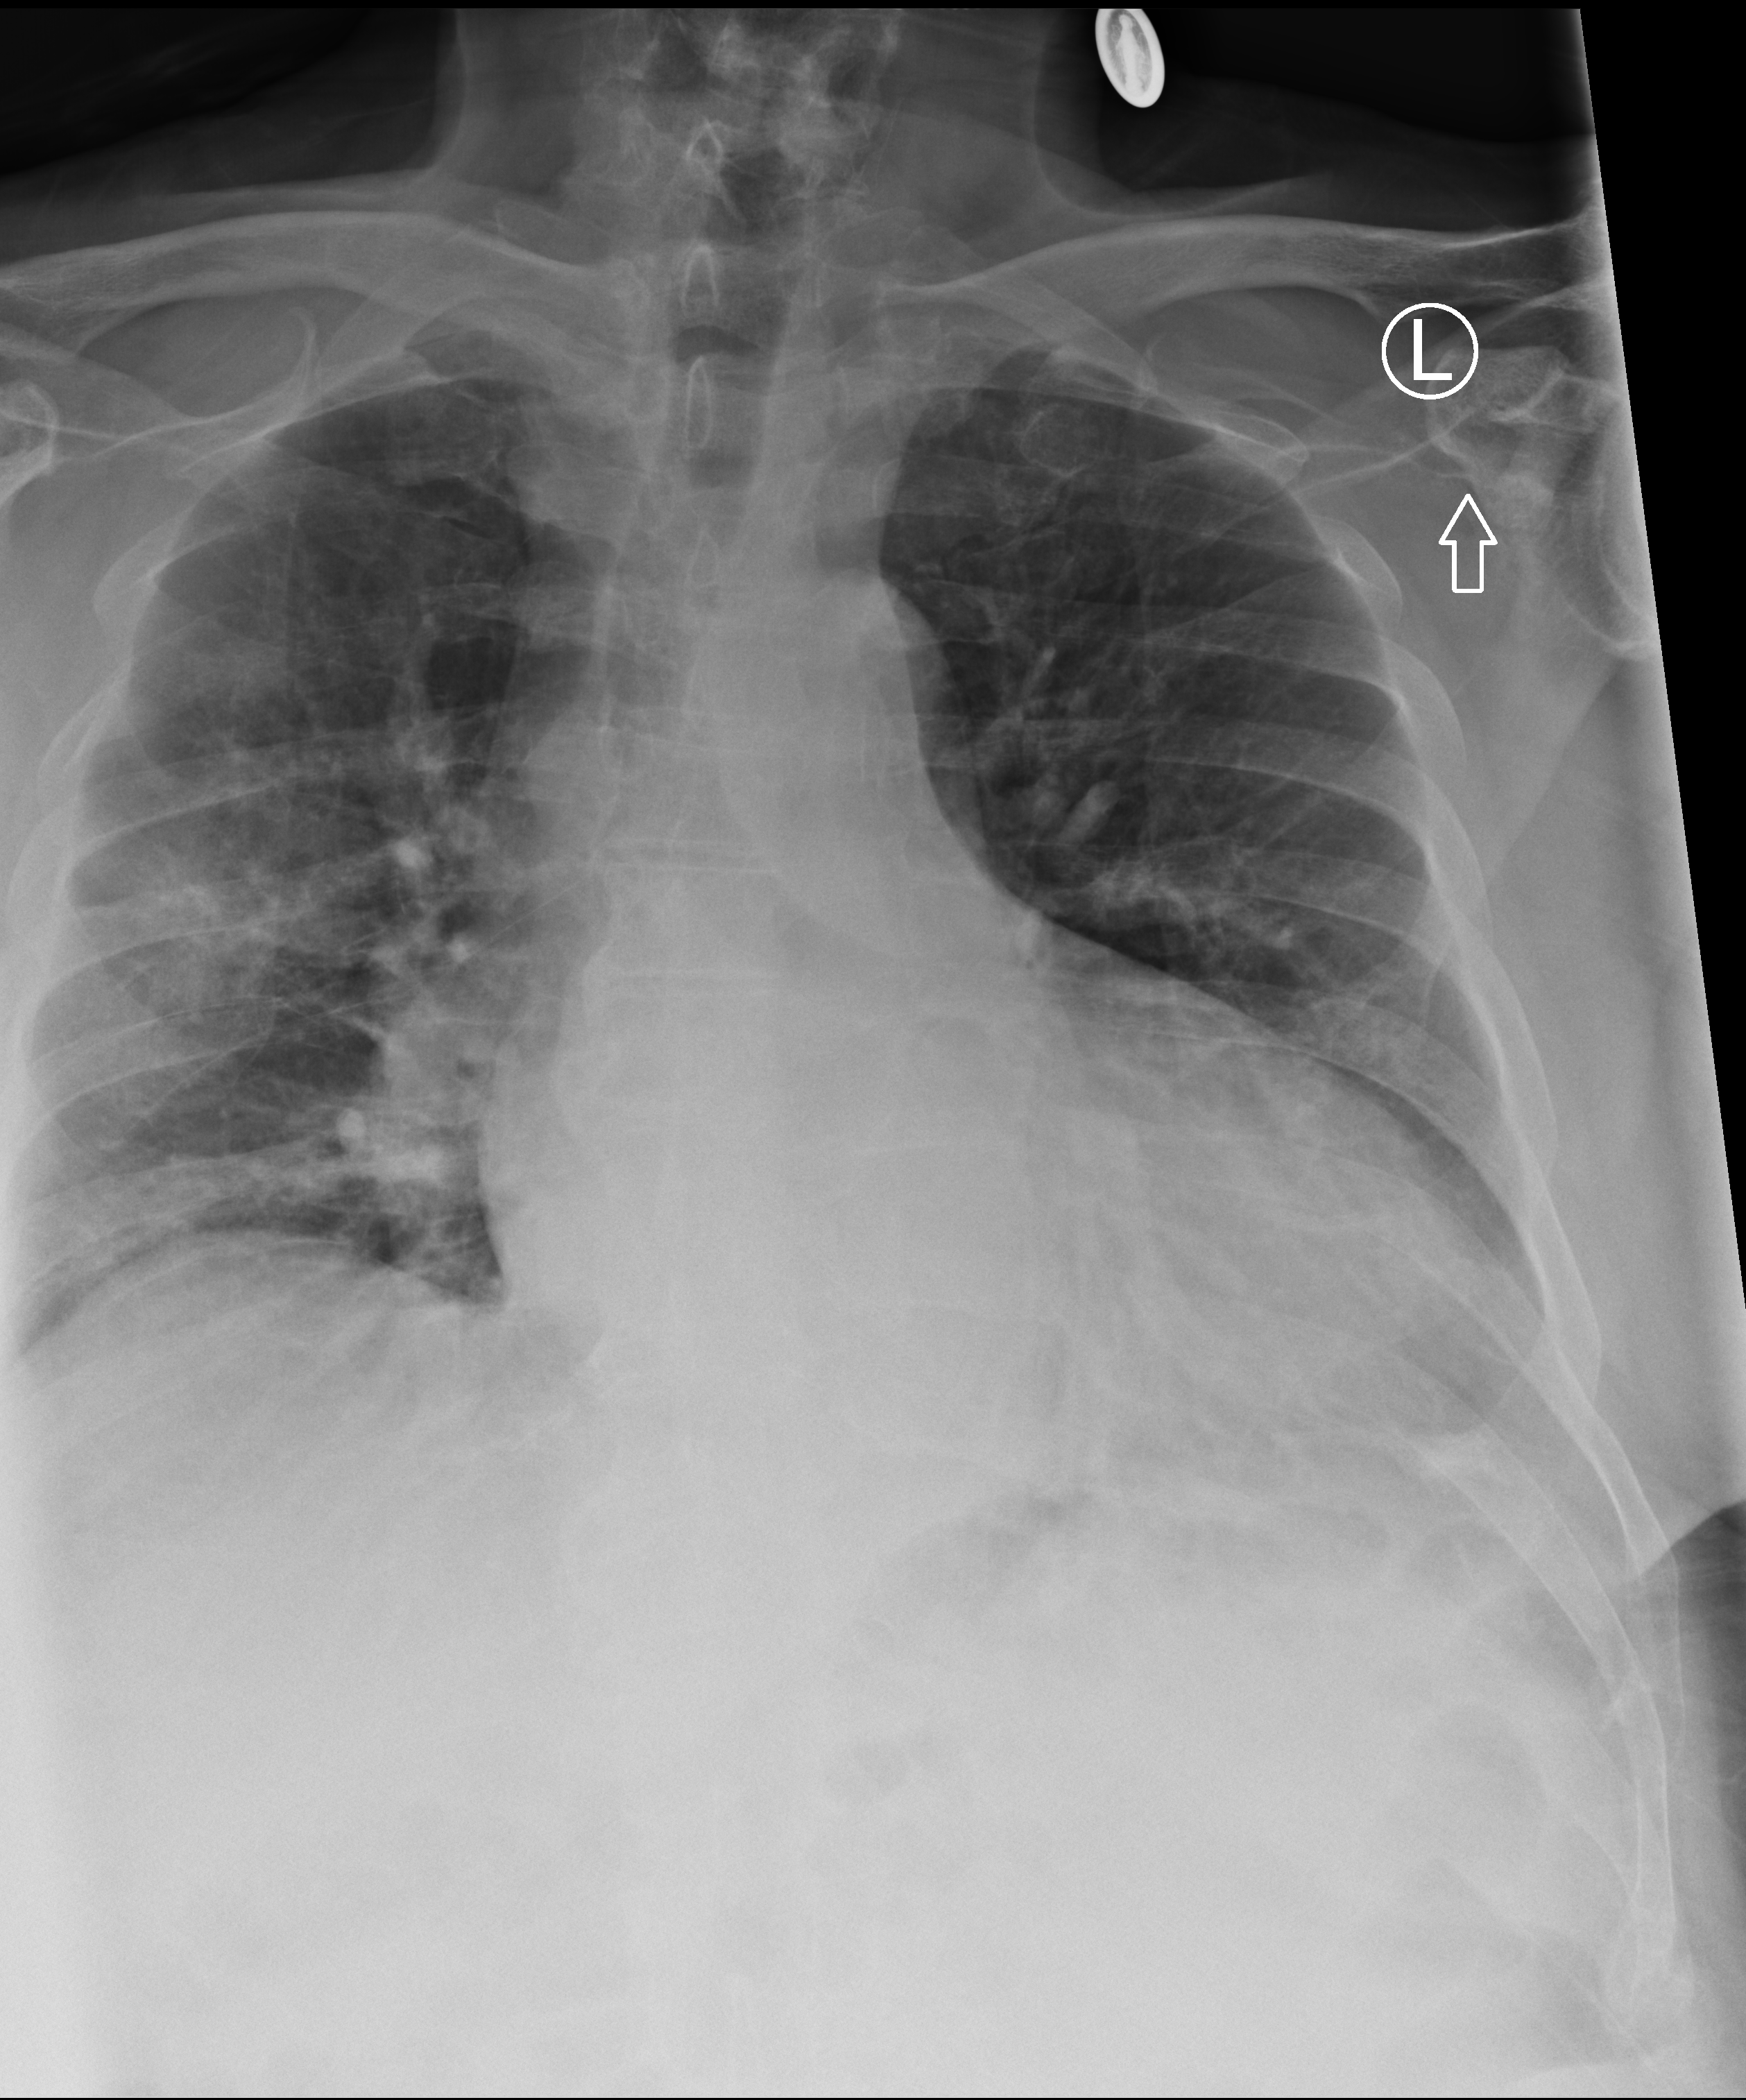
Portable chest radiograph, anteroposterior (AP) projection. Patient hospitalised with COVID-19; male, aged 75–90 years.
Admission-level facts for this patient (not findings on this image; timing relative to this image not recorded): admitted to intensive care during this hospital stay: no; diabetes (admission record): no.